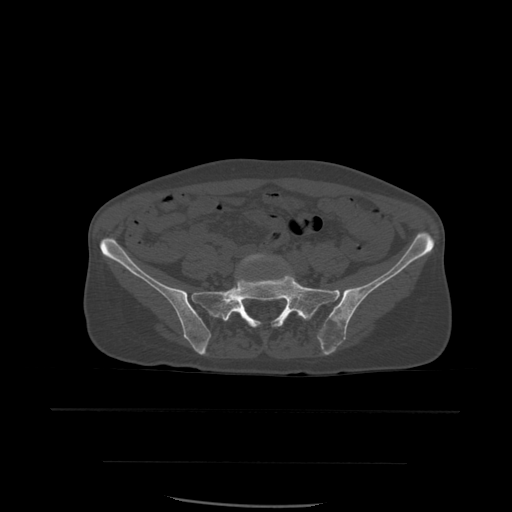
CT including the spine, one axial slice; slice 132 of 574 in the series (ordered by position); bone window (W 1800 / L 400 HU); 1.25 mm slice thickness; 512 × 512 image matrix, field of view 392 × 392 mm. Patient age 48 years. Case-level facts recorded for this patient, not image findings: primary cancer: lung.
Annotated regions visible in this slice (semi-automatically segmented with operator editing):
- L5 vertebra: bounding box (x1, y1, x2, y2) in pixels: (229, 253, 303, 318)